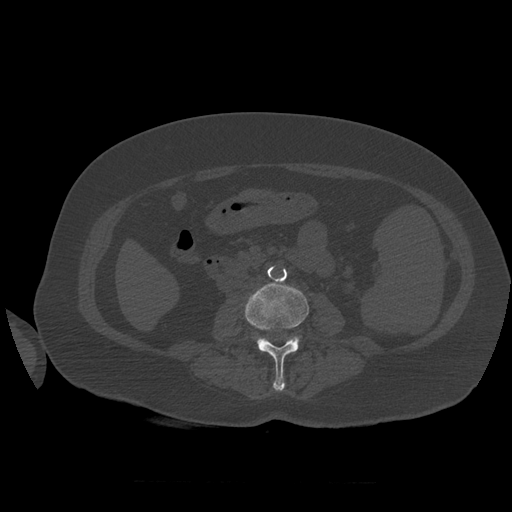
CT including the spine, one axial slice. Slice 225 of 399 in the series (ordered by position). Reconstruction kernel STANDARD. Bone window (W 1800 / L 400 HU). 512 × 512 image matrix, field of view 404 × 404 mm. Patient age 81 years. Case-level facts recorded for this patient, not image findings: primary cancer: renal; vertebrae with lytic lesions (as recorded): L1.
Annotated regions visible in this slice (semi-automatic segmentation, software-assisted and operator-edited):
- L3 vertebra: bounding box [x1, y1, x2, y2] px = [245, 283, 309, 391]